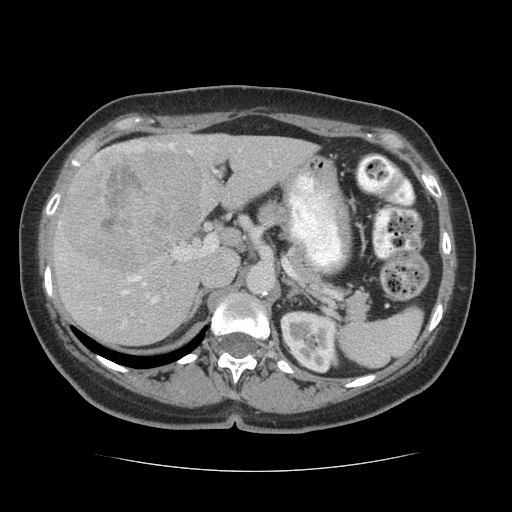
Contrast-enhanced abdominal CT (liver protocol), one axial slice; position 38 of 75 along the scan axis; soft-tissue window (W 400 / L 40 HU); 2.5 mm slice thickness; 512 × 512 image matrix. Case-level facts recorded for this patient, not image findings: diagnosis: hepatocellular carcinoma (patient treated with transarterial chemoembolisation; whether this scan precedes or follows treatment is not stated here); TNM stage (as recorded): Stage-I; Child-Pugh class: A.
Structures marked on this image (semi-automatically segmented with operator editing):
- liver parenchyma outside the tumour (the mass and vessels are separate outlines, so this box may not span the whole liver): bounding box (x1, y1, x2, y2) in pixels: (52, 132, 316, 344)
- mass: (63, 146, 202, 274)
- liver vessels: (58, 143, 240, 324)